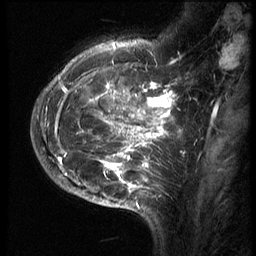
Breast MRI (dynamic contrast-enhanced), one sagittal slice. Slice 21 of 70 in the series (ordered by position). 3 images stored at this slice position (order not interpretable as contrast timing). 1.5 T. TE 4.2 ms, TR 9 ms. 2.5 mm slice thickness. 256 × 256 image matrix. Female patient, age 28 years. Case-level facts recorded for this patient, not image findings: setting: breast cancer imaged before/during neoadjuvant chemotherapy.
Outlined on this slice (semi-automatic segmentation, software-assisted and operator-edited):
- analysis volume of interest (the breast-tissue region the enhancement analysis was run in; not a lesion): bounding box <43,42,186,215> (left, top, right, bottom; pixels)
- tumour enhancement mask (voxels above the 140 % enhancement threshold inside the analysis volume of interest): <56,55,179,194>